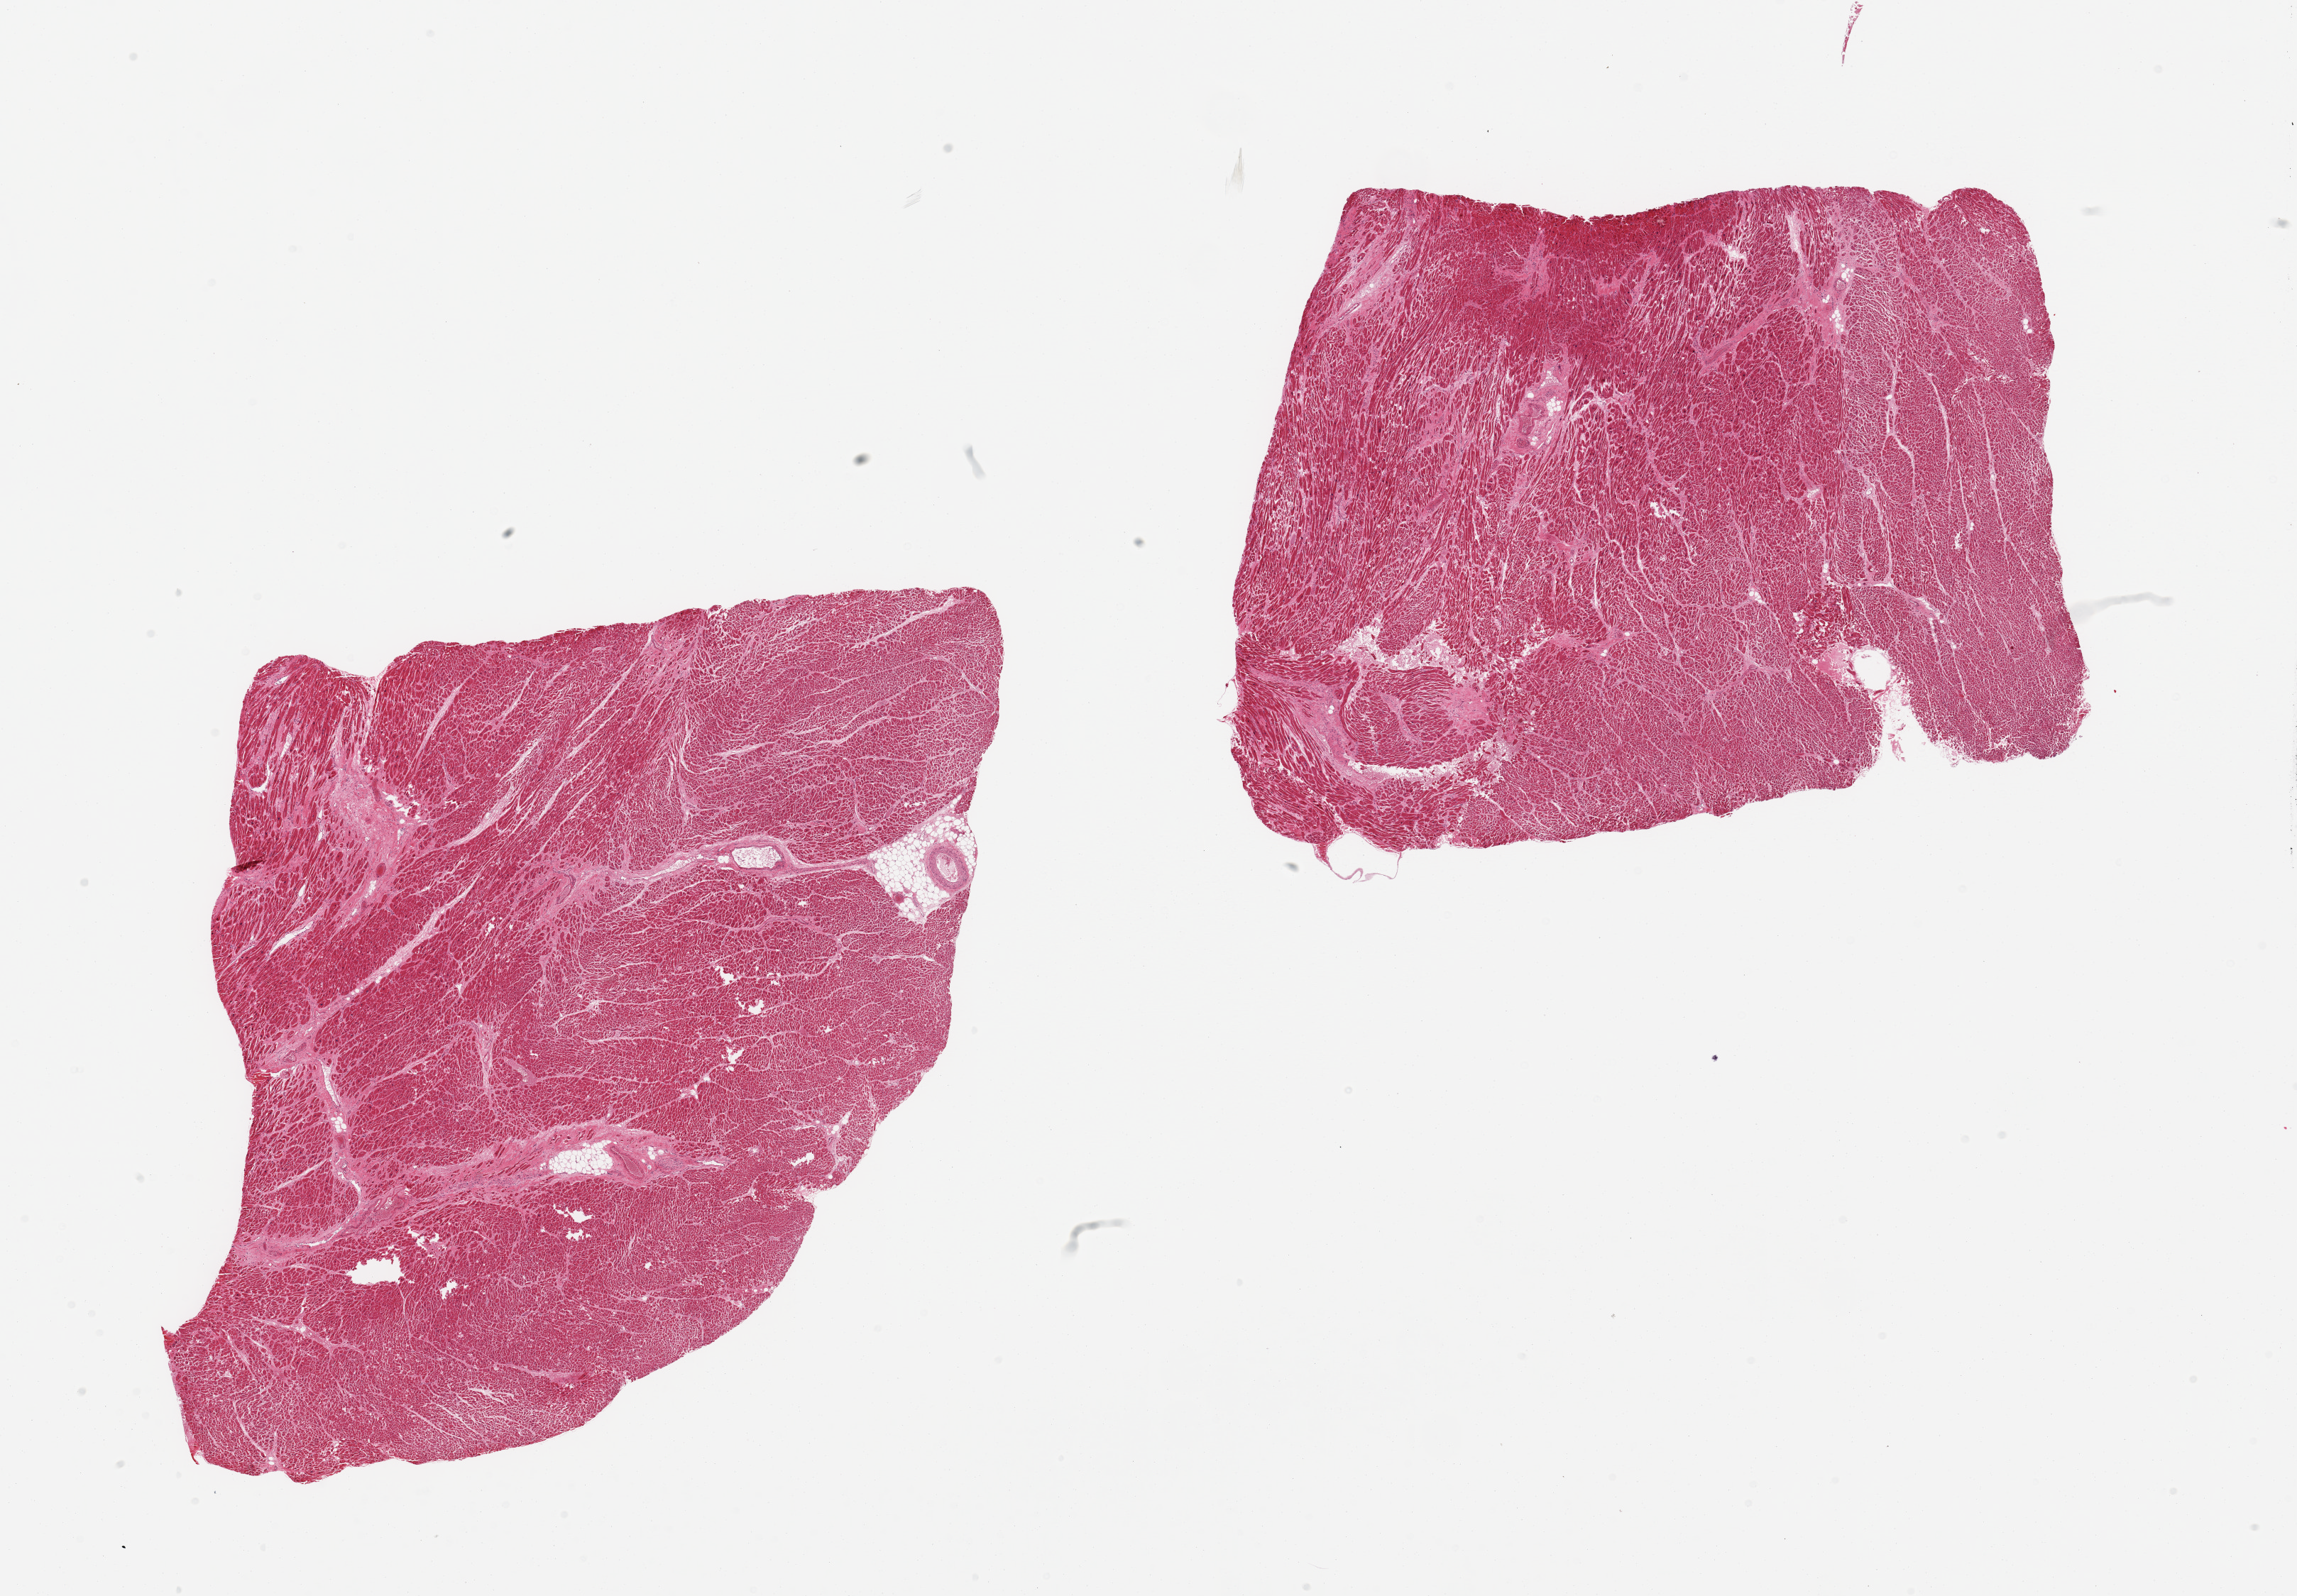
H&E whole-slide image, a low-resolution overview of the entire scanned area, about 25.6 x 17.8 mm (acquisition: 20x scan). PAXgene-fixed paraffin-embedded (PFPE) section. Sampled site (target tissue): heart. Tissue donor sample.
- reviewer comment on this tissue sample: 2 pieces chronic ischemic changes,interstitial fibrosis, focal microinfarcts